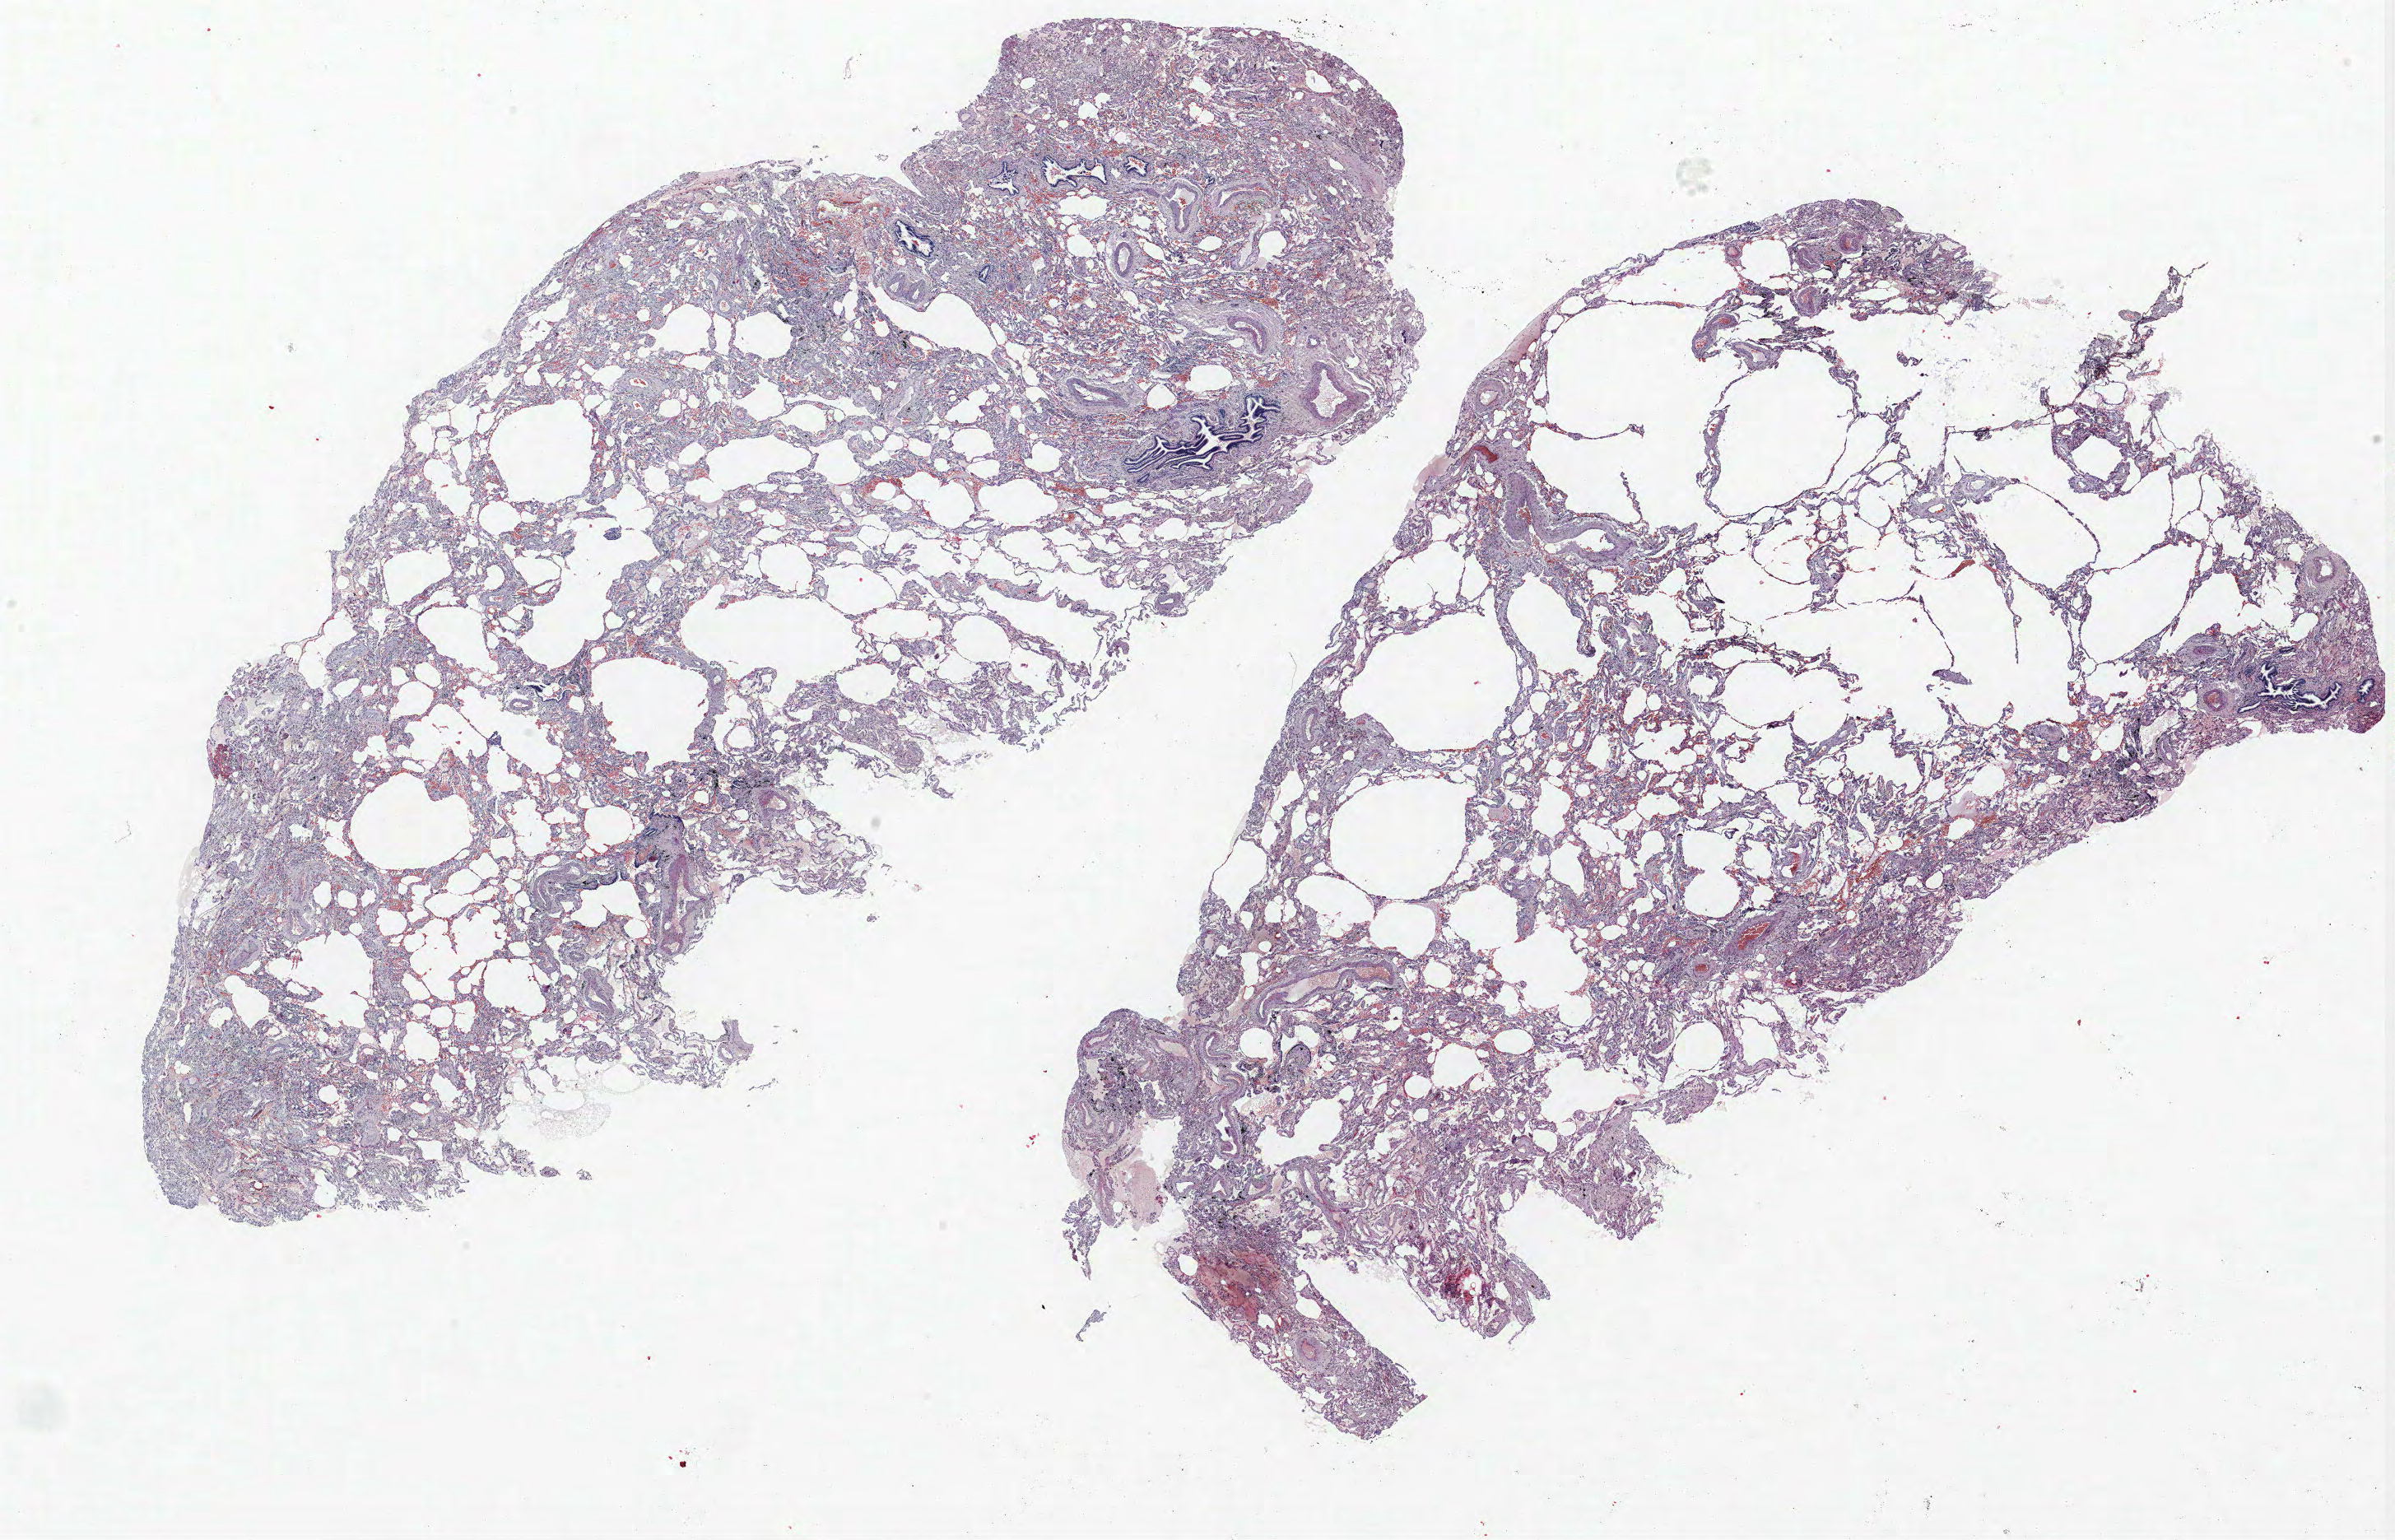
Whole-slide histology image, H&E-stained, whole scanned area (about 23.3 x 15.0 mm) shown as a low-resolution overview, formalin-fixed paraffin-embedded (FFPE) section, lung tissue. Male, age 67 at enrolment. Former smoker at enrolment.
Participant's lung-cancer diagnosis: Squamous cell carcinoma, NOS (ICD-O-3 8070/3).